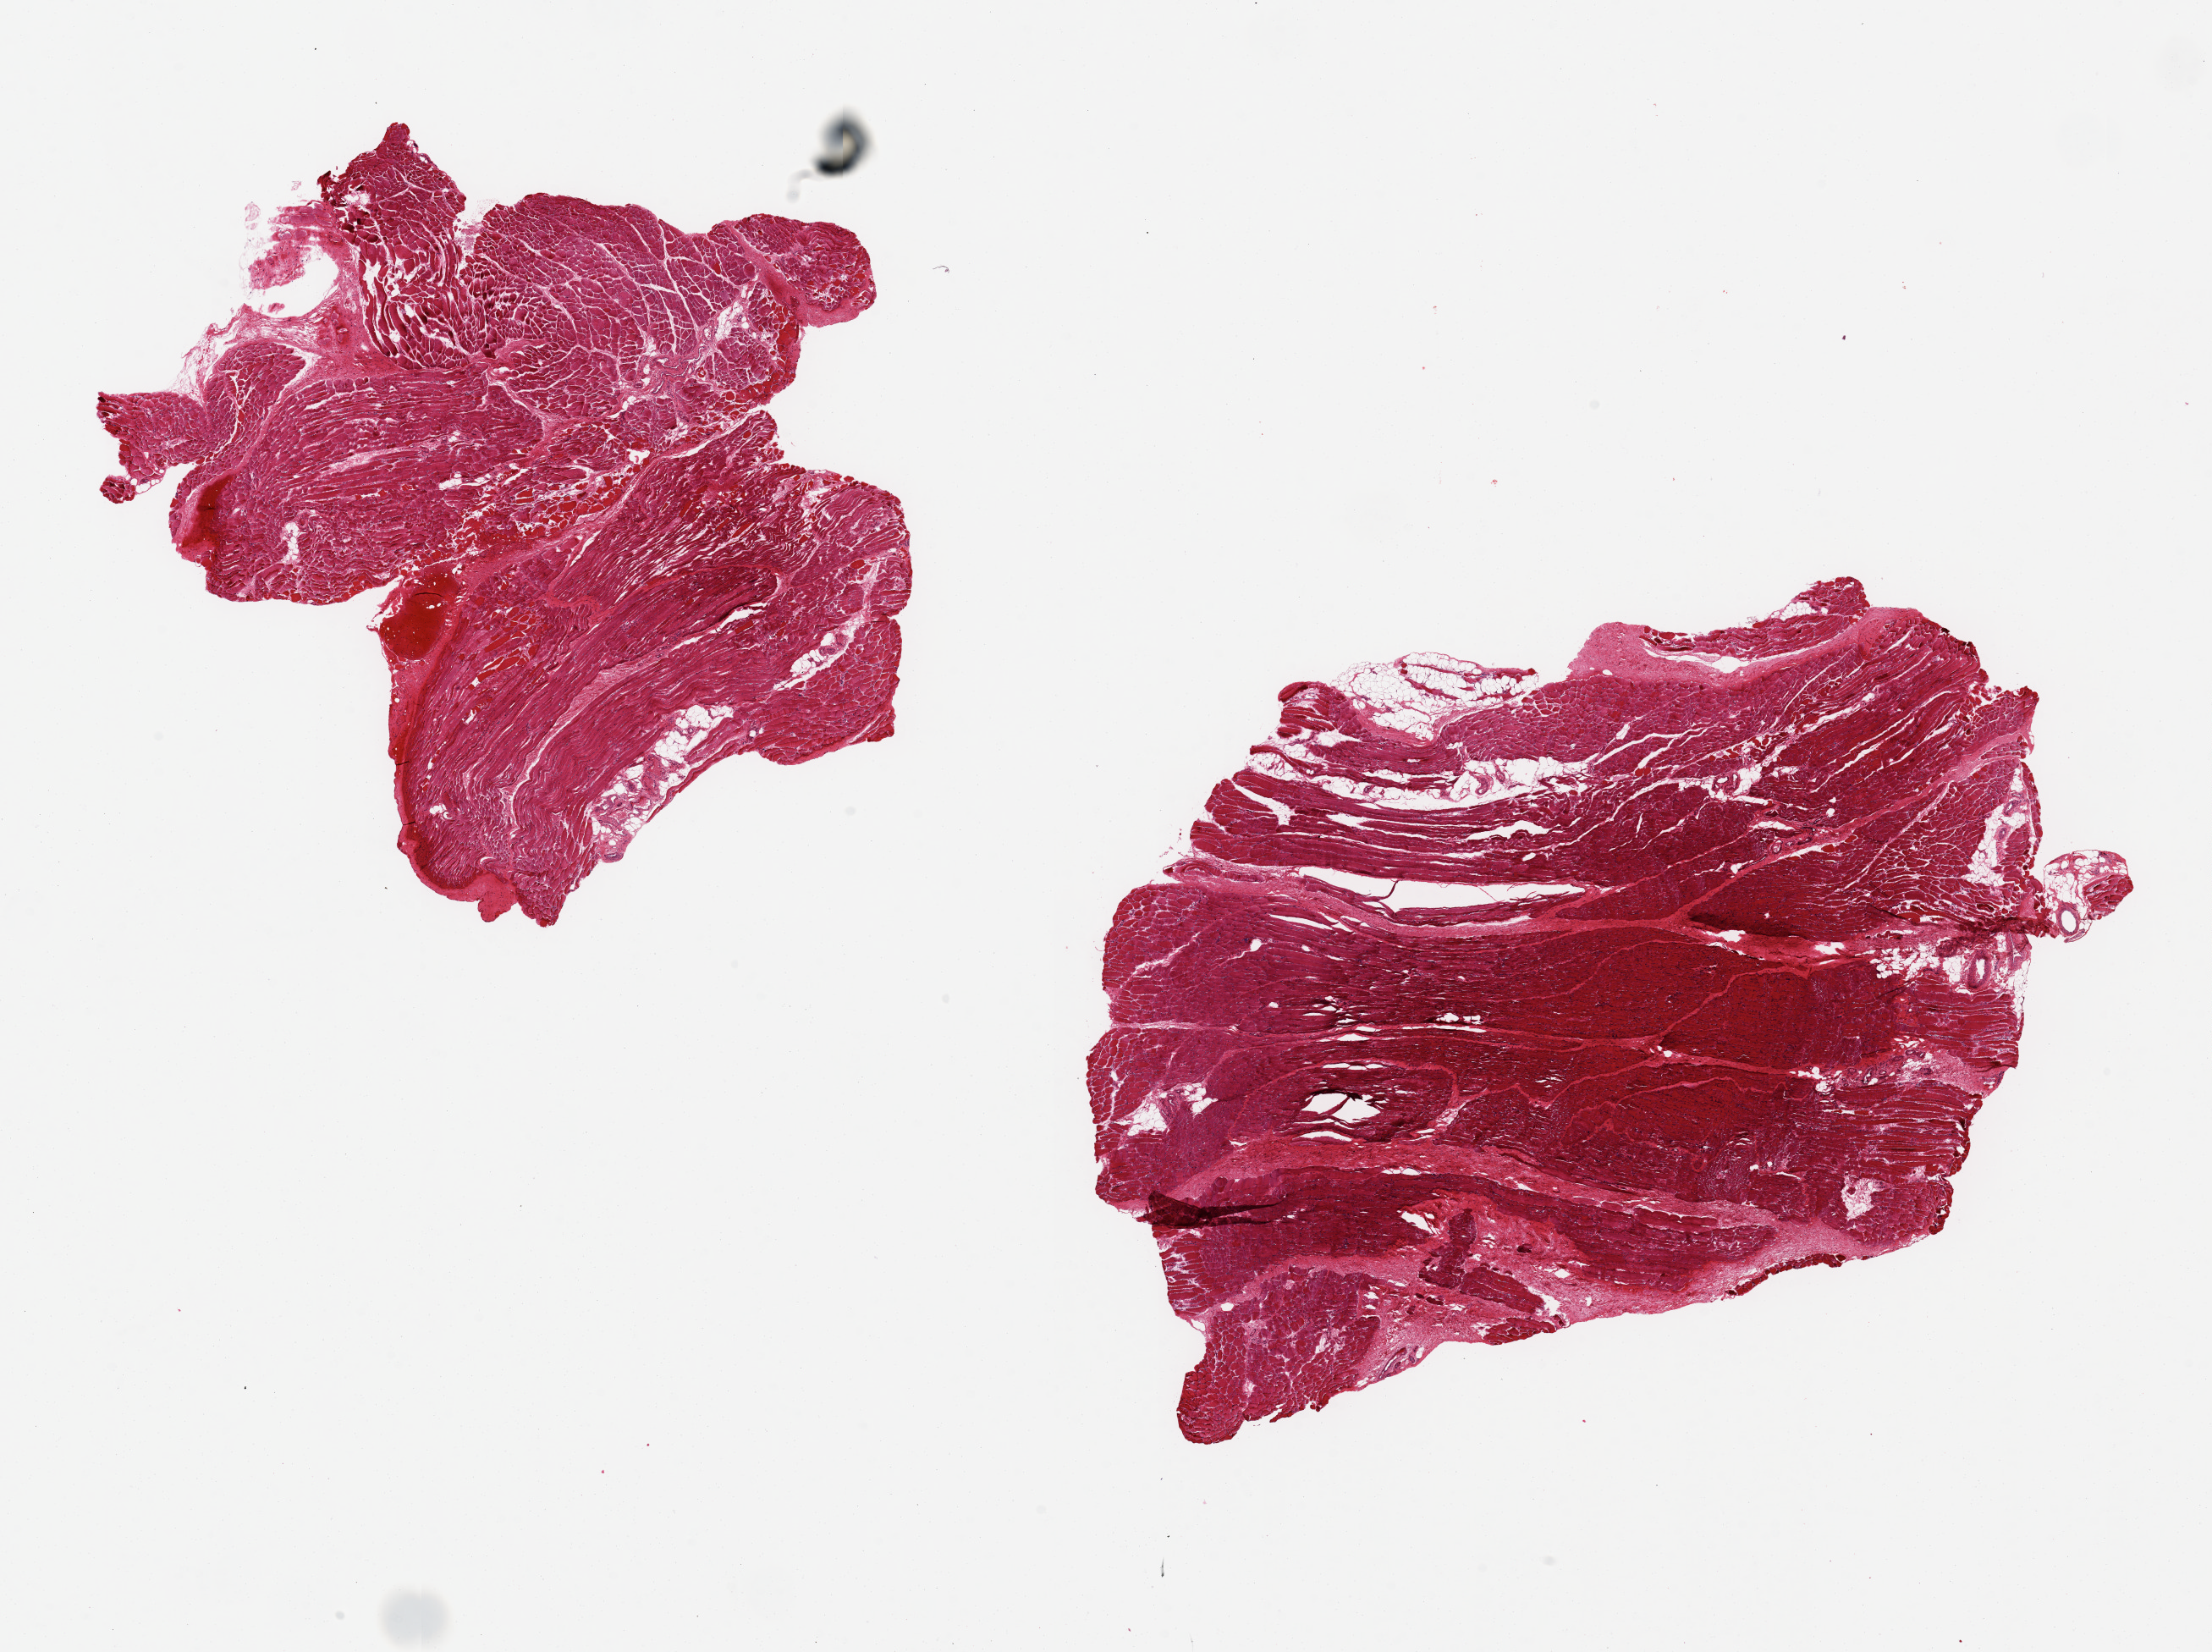
Whole-slide image, H&E stain — shown as a low-resolution overview of the whole scanned area (about 20.7 x 15.4 mm); PAXgene-fixed paraffin-embedded (PFPE) section; section of skeletal muscle (target tissue); donor tissue sample. Donor sex: male.
Reviewer comment on this tissue sample: 2 pieces ~8x7mm; Prominent band of scarring/fibrosis, largest confluent focus ~1.5x1mm in one aliquot, ~15 % of specimen.